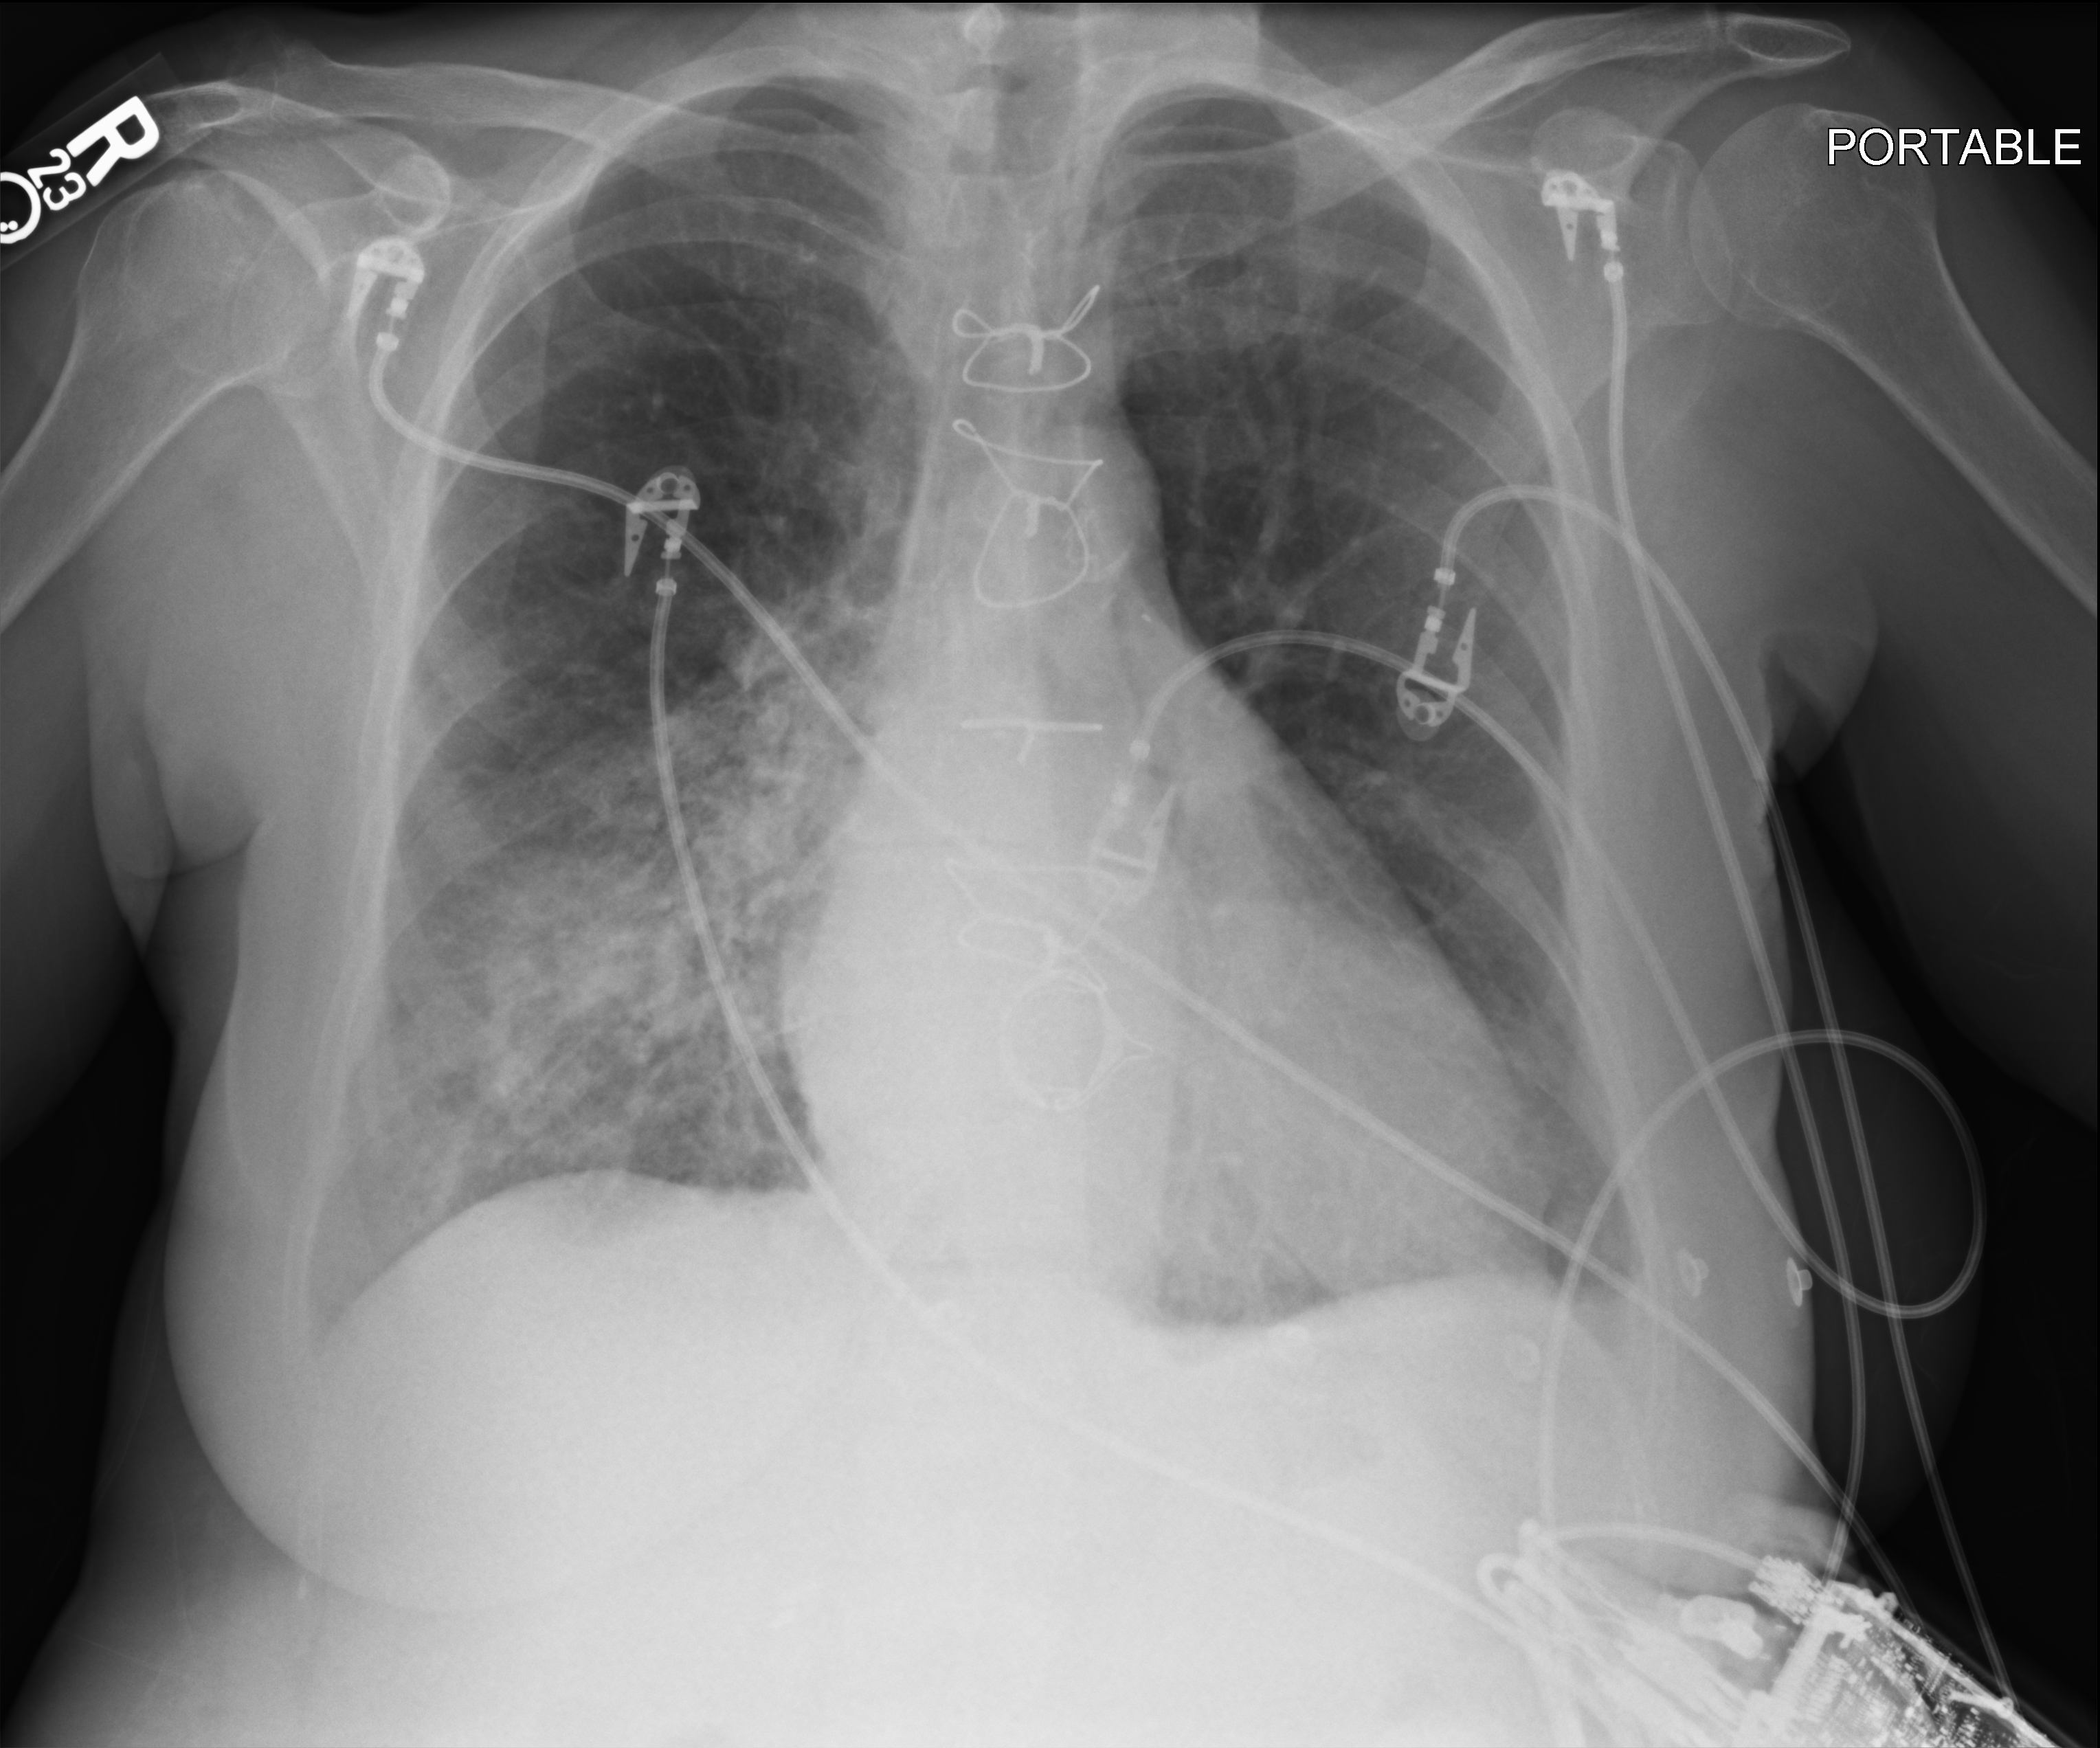
Bedside chest radiograph (computed radiography). Patient hospitalised with COVID-19; female, aged 60–74 years.
From the hospital-stay record, not from the radiograph (when in the stay this image was taken is not recorded):
- admitted to intensive care during this hospital stay: yes